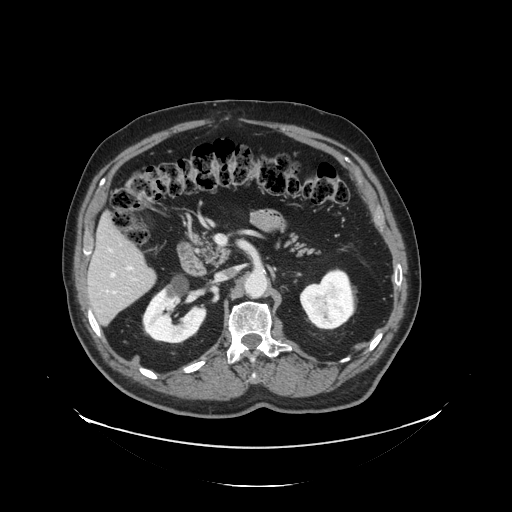
Contrast-enhanced abdominal CT, one axial slice; position 65 of 138 along the scan axis; reconstruction kernel STANDARD; 120 kVp; intravenous contrast given; soft-tissue window (W 400 / L 40 HU); 512 × 512 image matrix, field of view 497 × 497 mm. Male patient, age 77 years. Case-level facts recorded for this patient, not image findings: diagnosis: colorectal cancer liver metastases, imaged before liver resection; multiple liver metastases: no; largest metastasis: 1.5 cm; disease in both lobes: no.
Annotated regions visible in this slice (manually delineated by an expert):
- liver: box from (x=90, y=218) to (x=155, y=325) px
- planned liver remnant (the part of the liver to remain after resection): (x=90, y=218)–(x=148, y=286)
- portal vein (with intrahepatic branches): (x=114, y=268)–(x=131, y=293)